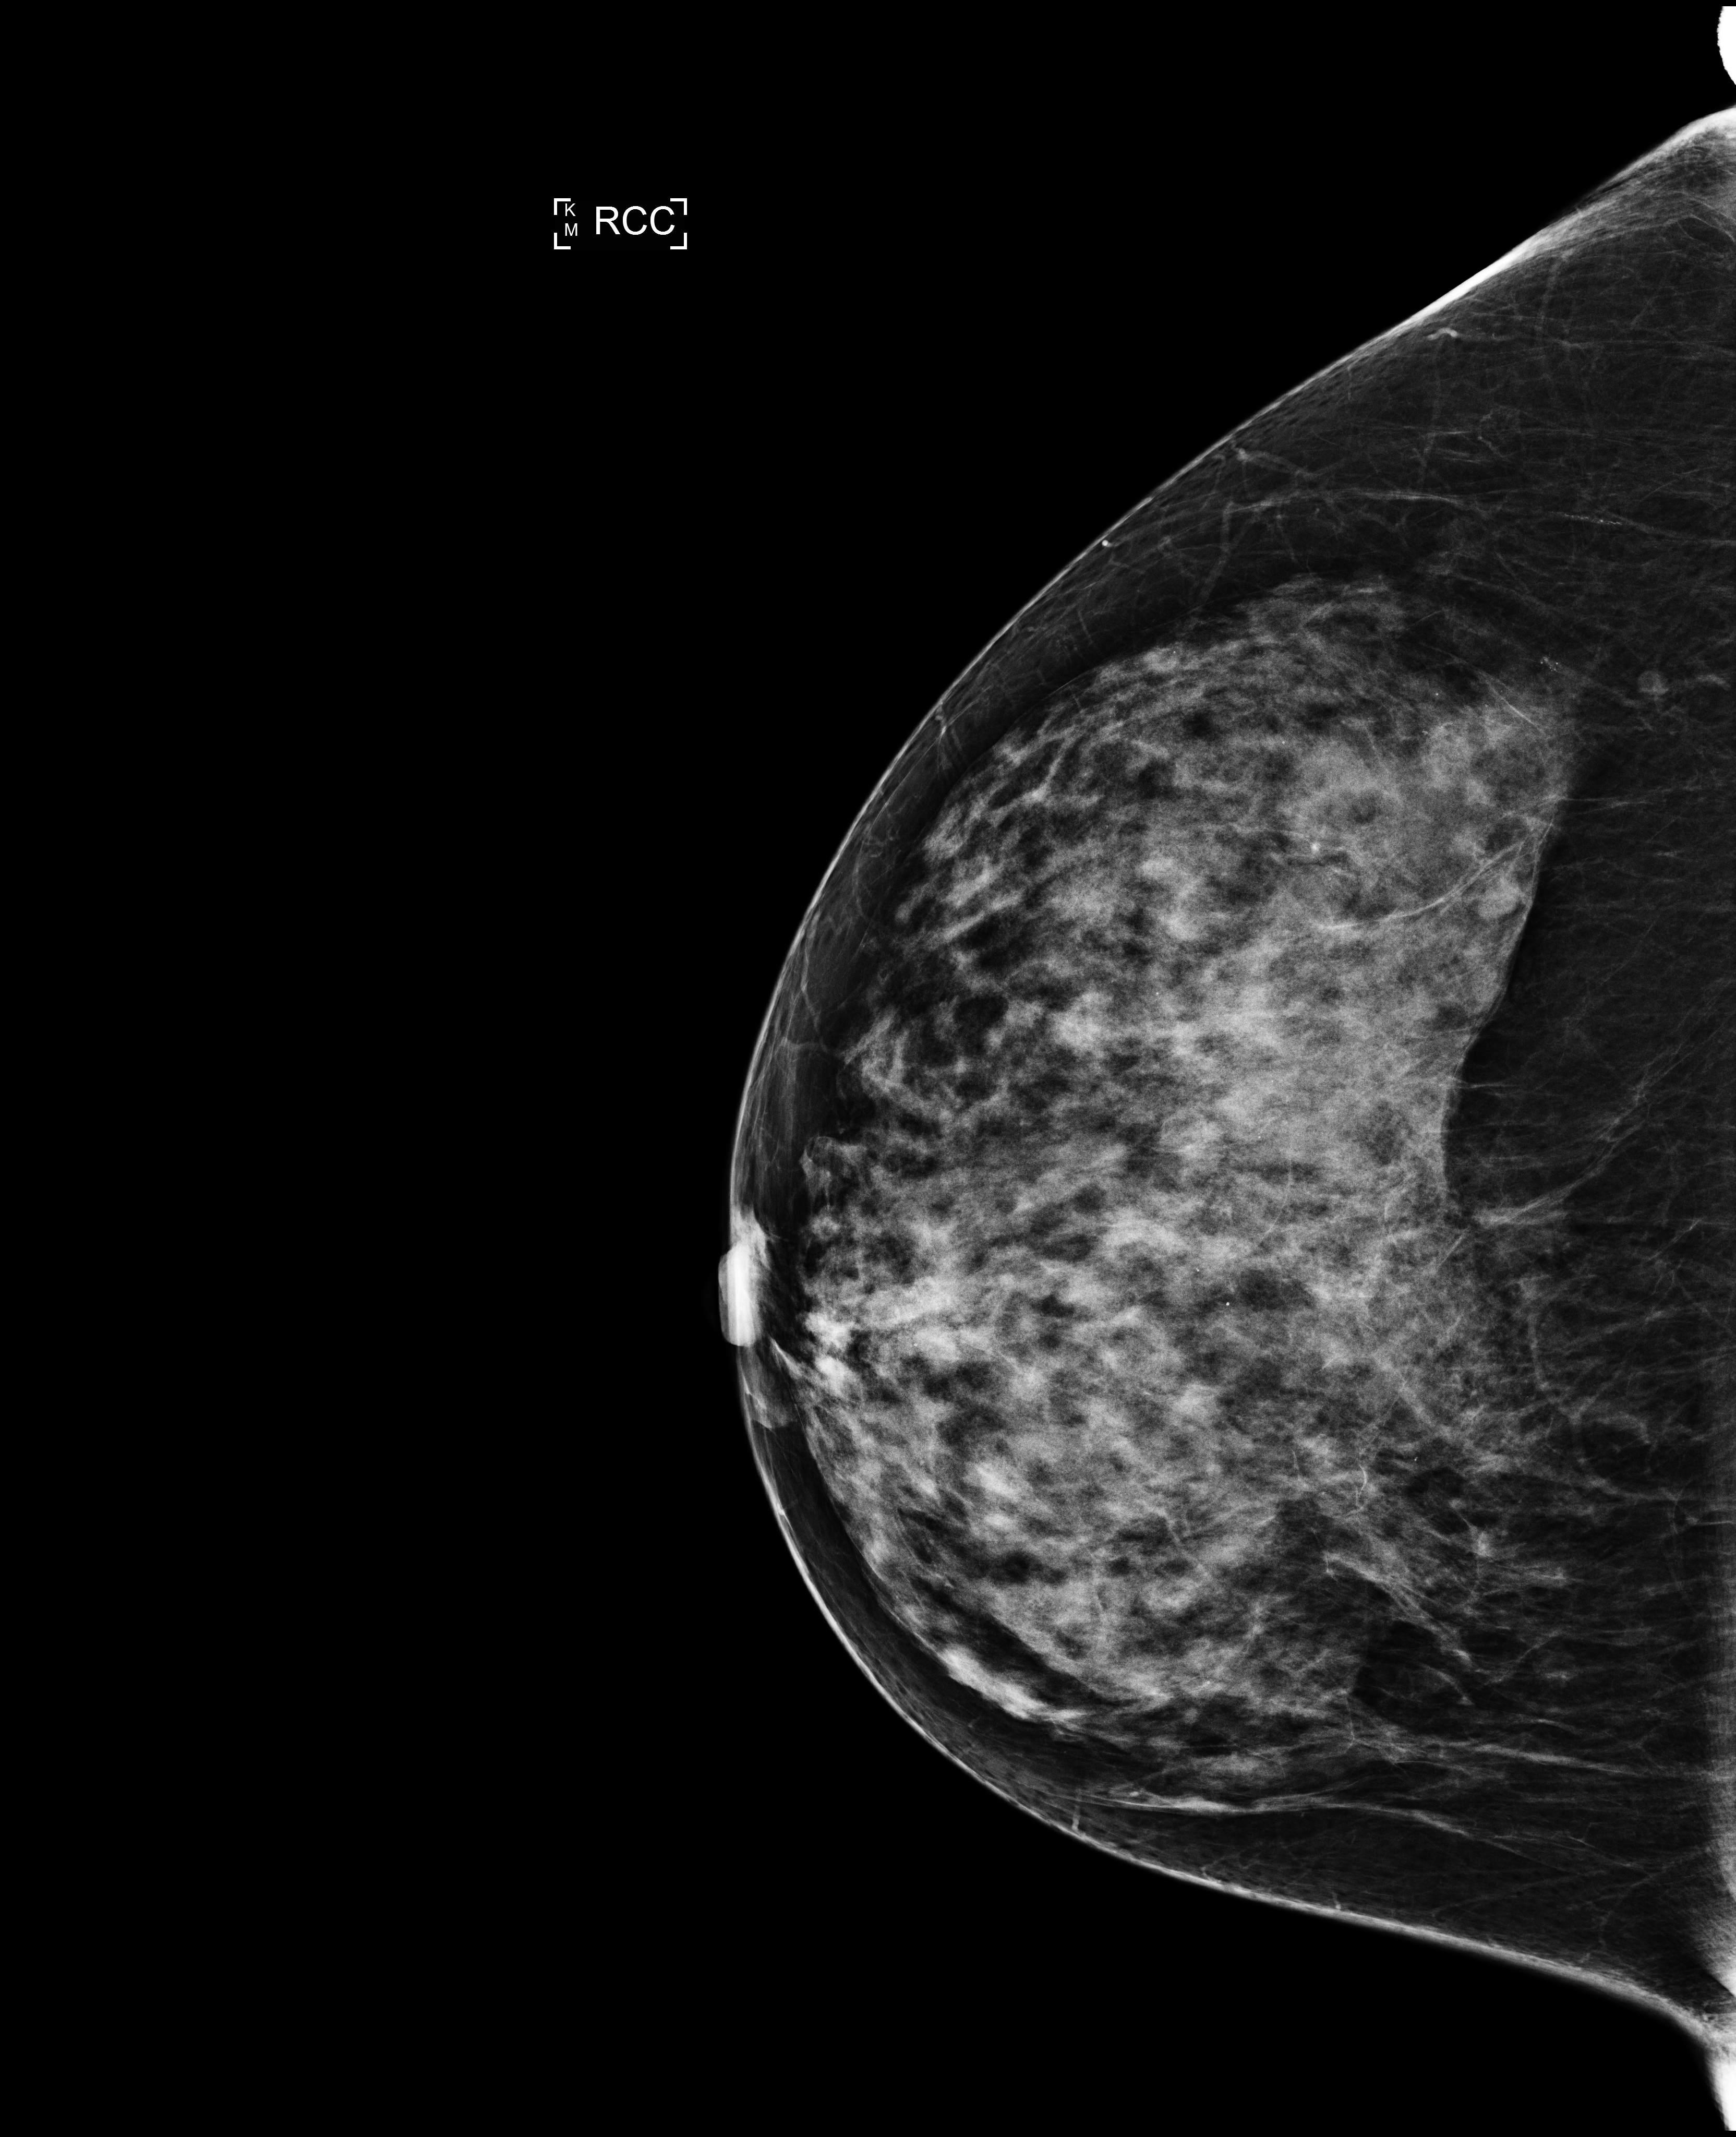
Full-field digital mammogram (FFDM), right breast, CC view, screening examination, compressed breast thickness 54 mm, system: Selenia Dimensions. Female patient, age 56 years.
- BI-RADS breast density category at the screening exam (both breasts, scale 1–4): 4
- final BI-RADS category for the screening round (tomosynthesis exam, both breasts): category 2
- recall: no recall after this screen